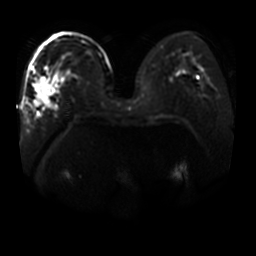
Breast MRI, one axial slice. Slice 22 of 44 in the series (ordered by position). Diffusion-weighted series; image 2 of 4 stored at this slice position (different b-values; order by instance number). 3 T. 256 × 256 image matrix, field of view 400 × 400 mm. Female patient.
Outlined on this slice (manually delineated by an expert):
- tumour on diffusion-weighted imaging: bounding box <35,77,55,106> (left, top, right, bottom; pixels)